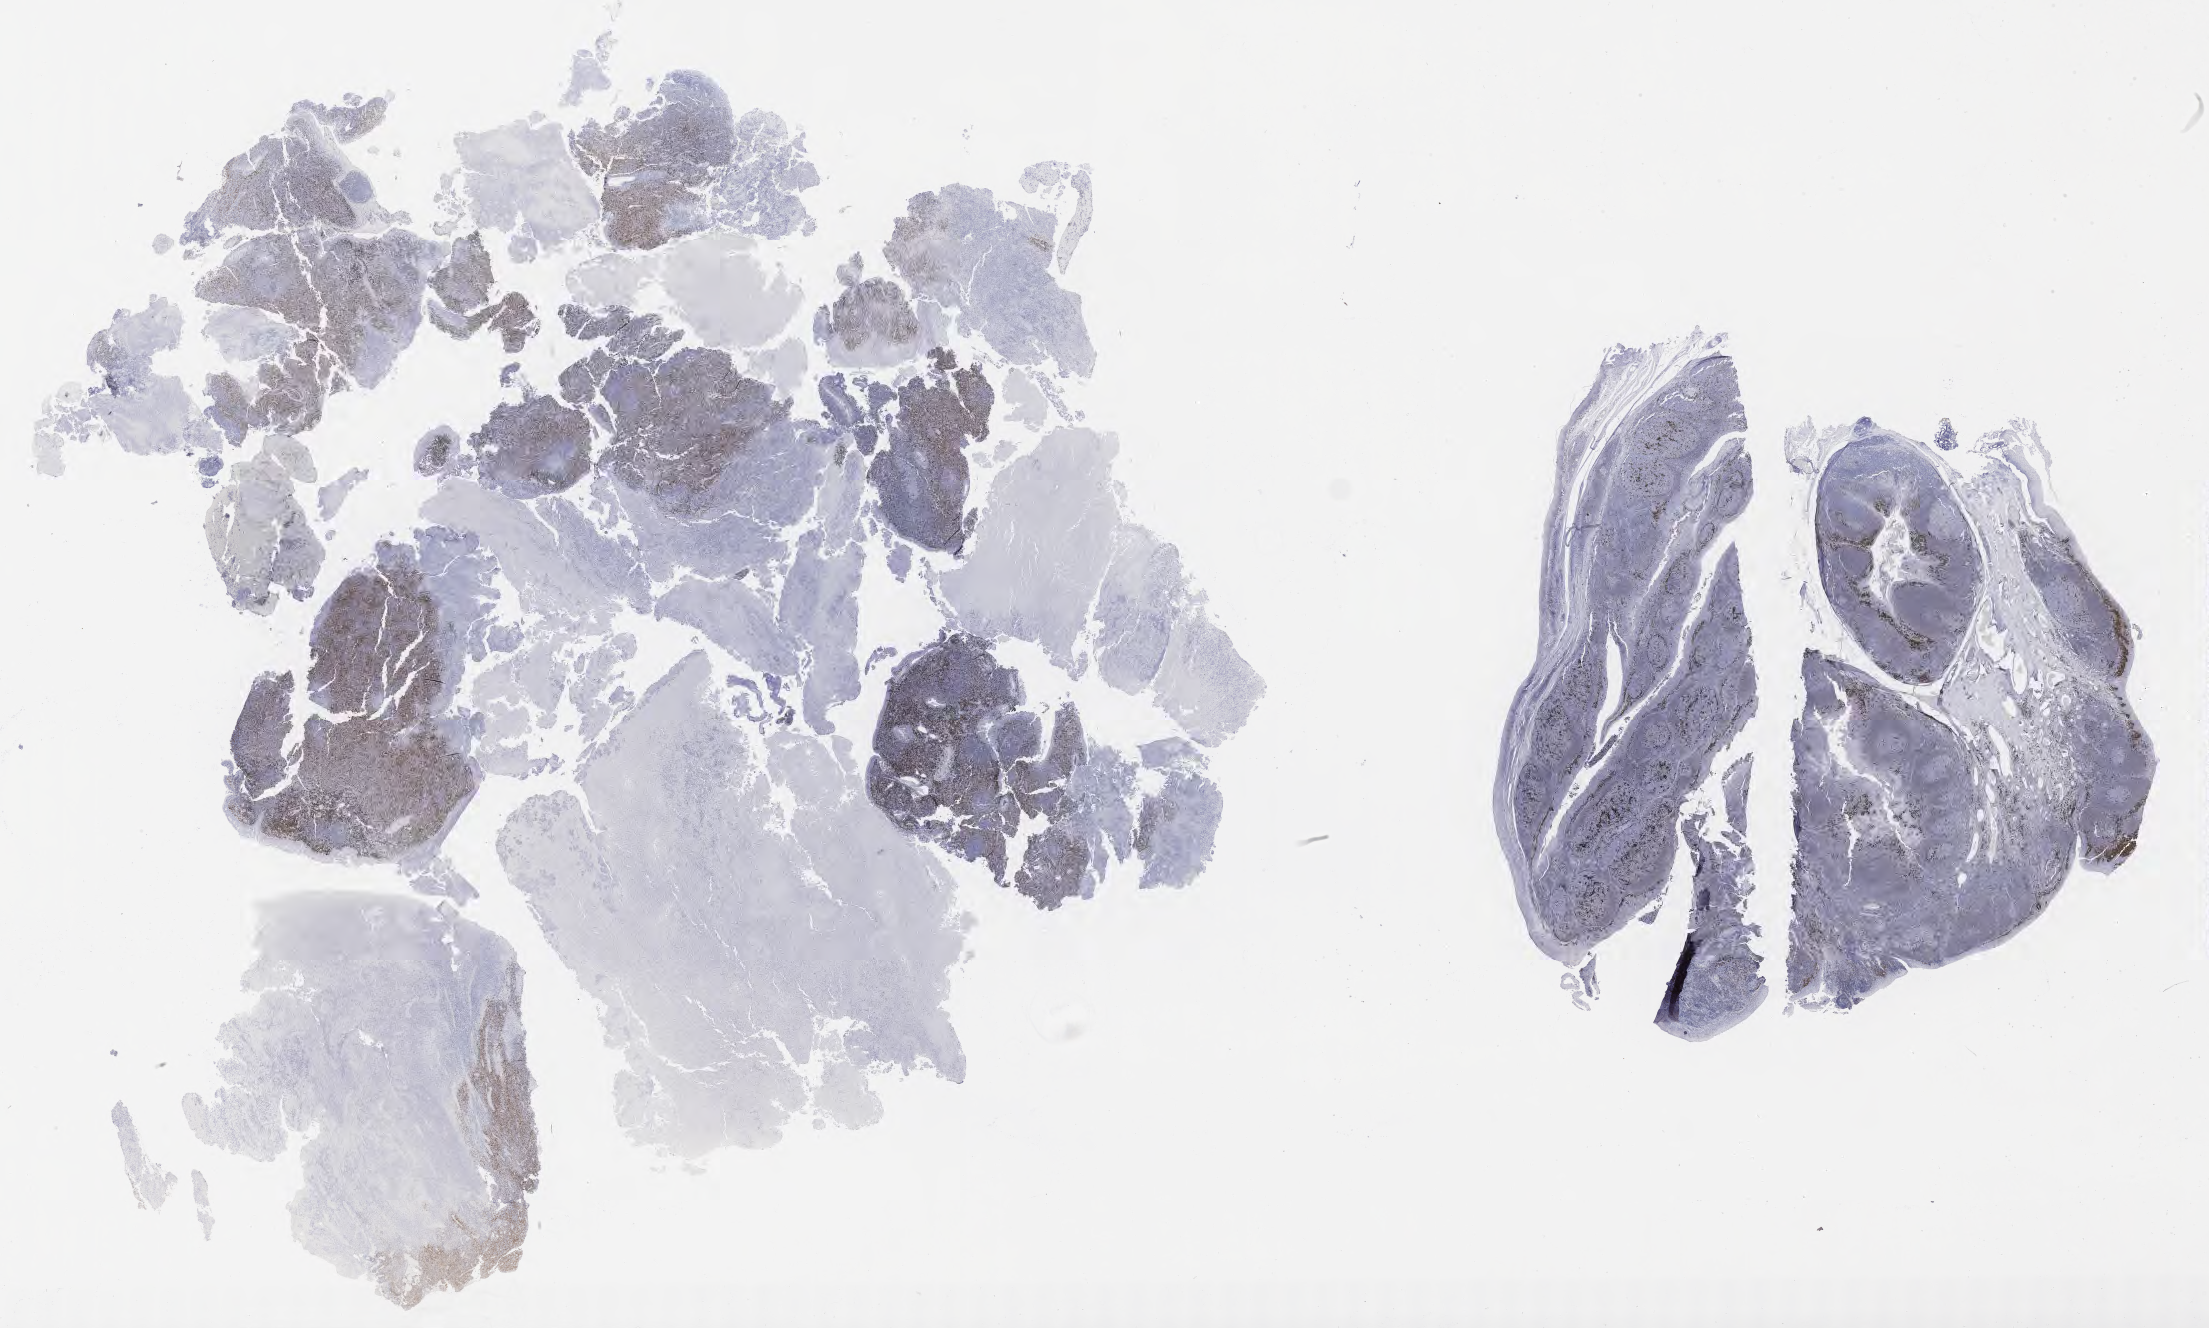
Immunohistochemistry (IHC) whole-slide image stained for IRF4/MUM1, shown as a low-resolution overview of the whole scanned area (about 35.7 x 21.5 mm); tumor tissue. Patient male; 47 years old.
Diagnosis: Diffuse large B-cell lymphoma, NOS.